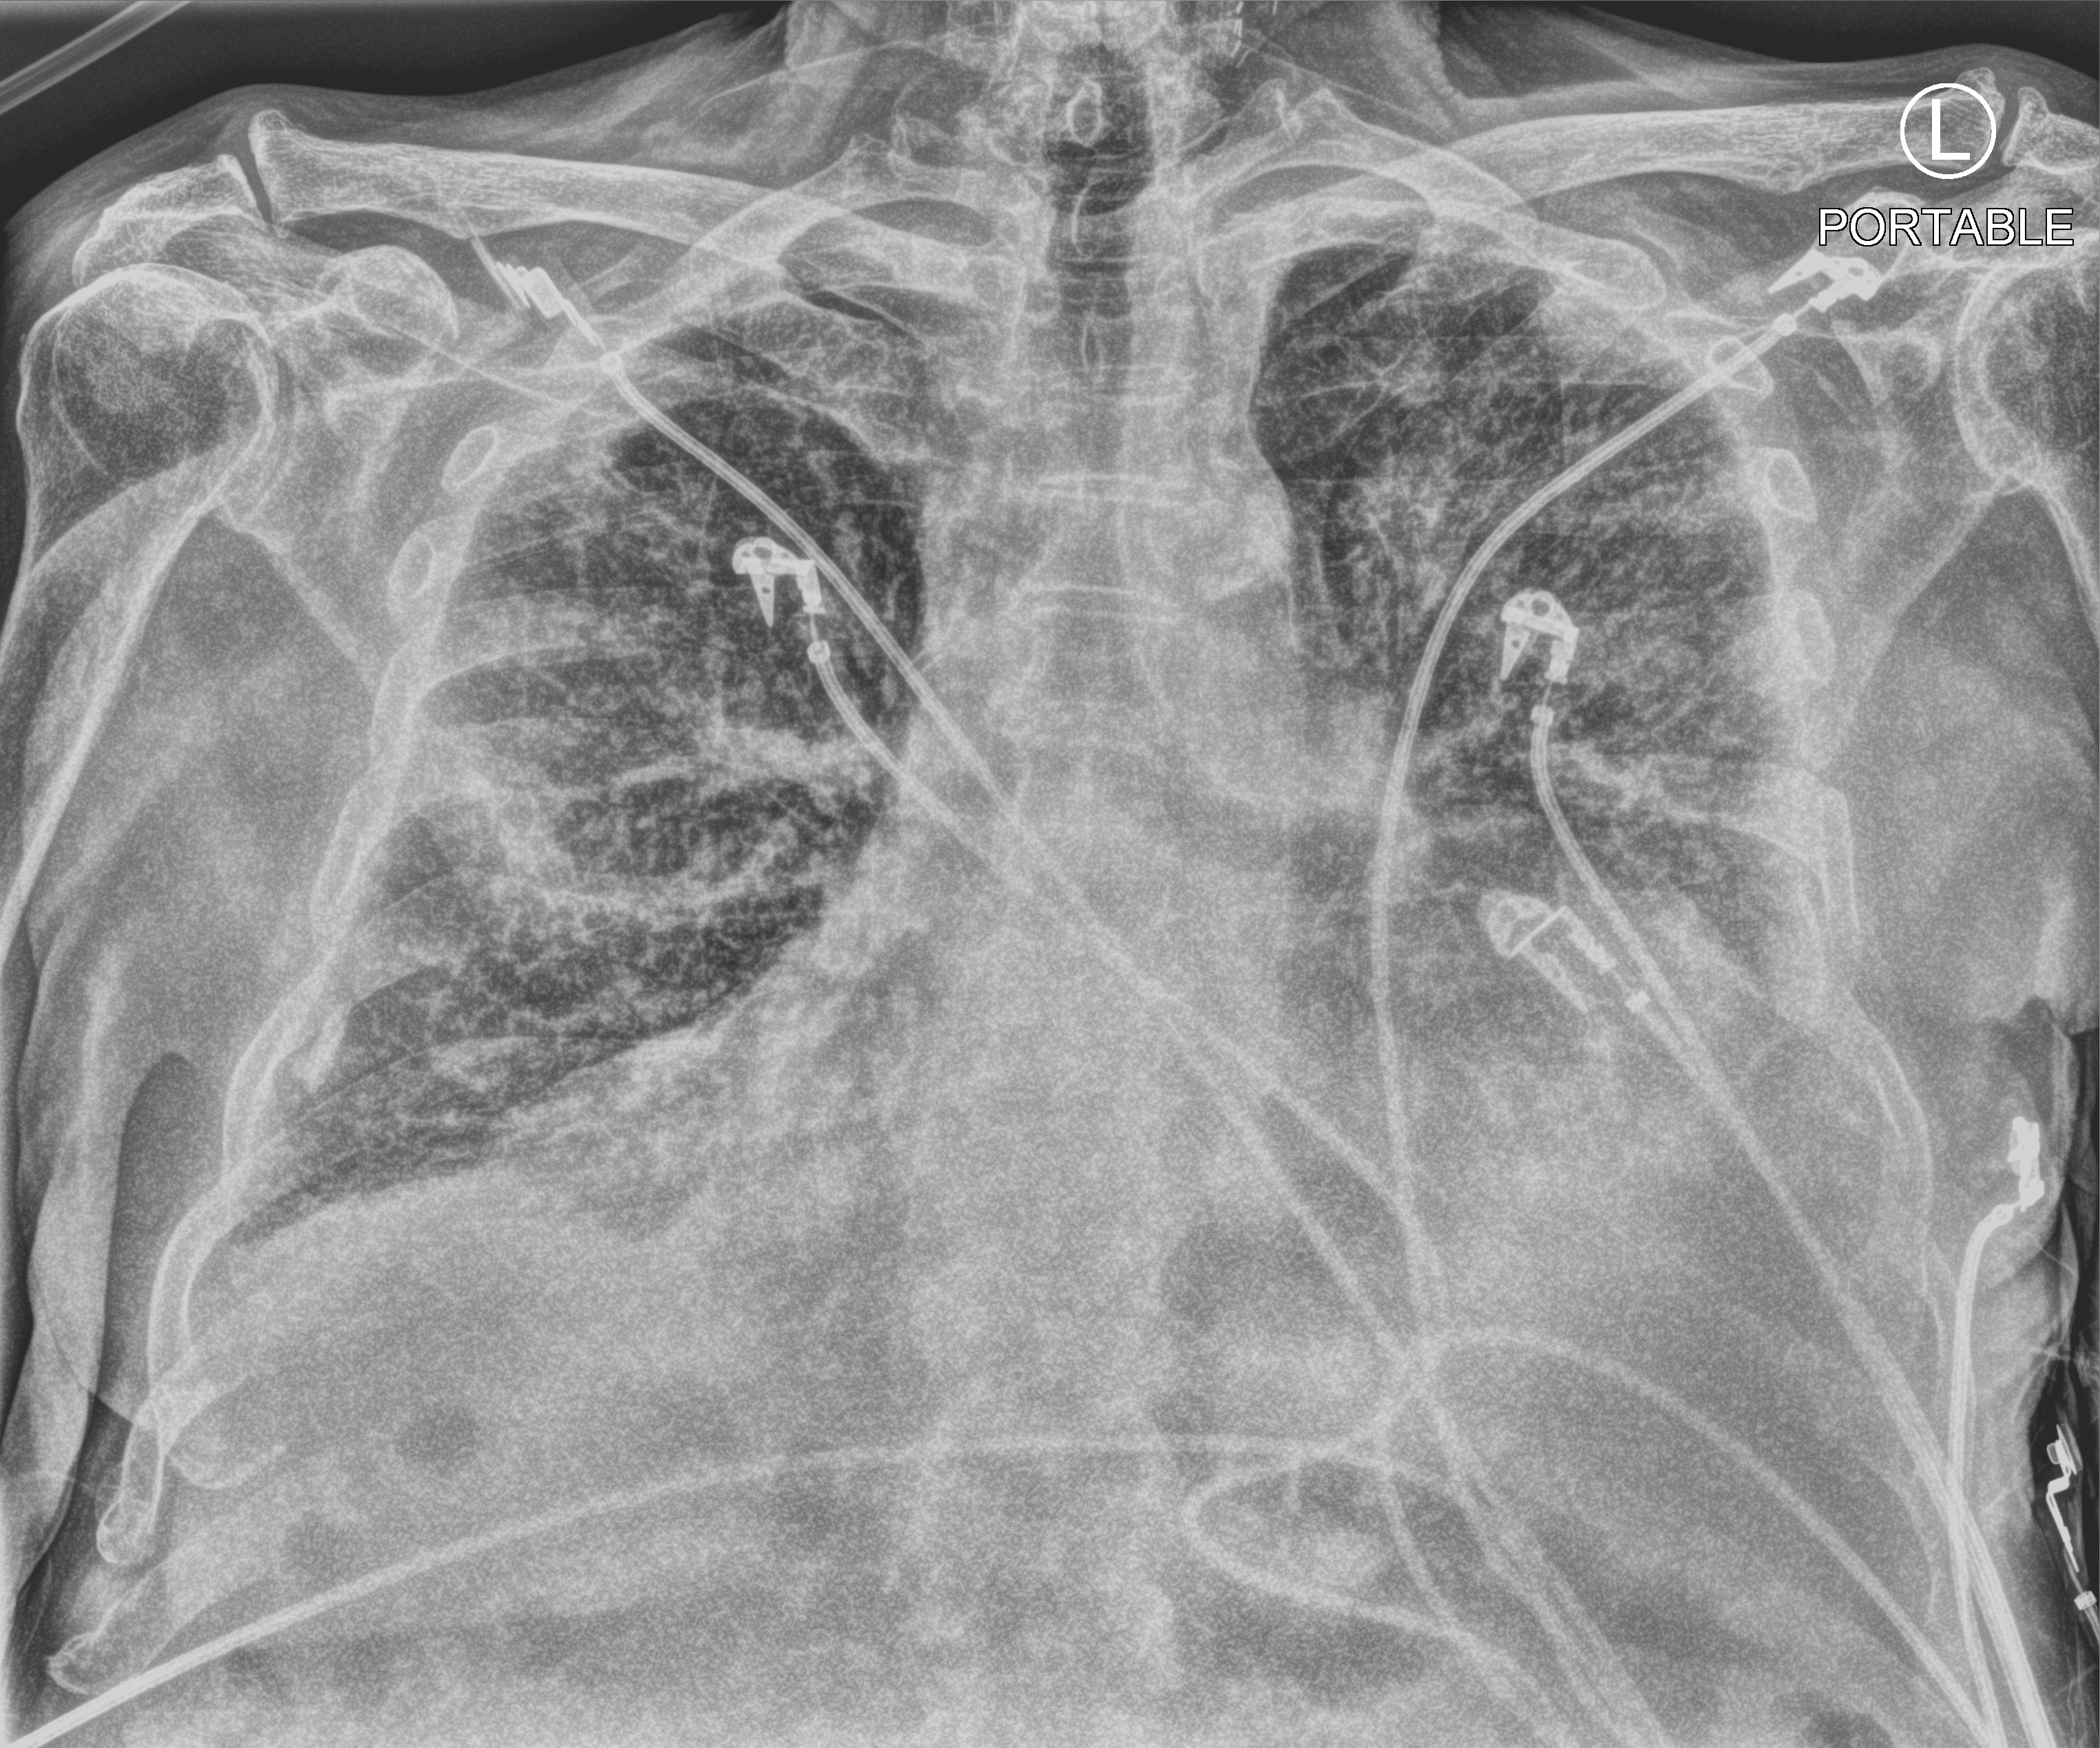
Chest X-ray (portable); anteroposterior (AP) projection. Male patient hospitalised with COVID-19, age 75–90 years.
Hospital-stay facts (about this admission, not read from this image; timing relative to this image not recorded): length of hospital stay: 6 days; mechanically ventilated during this hospital stay: yes.